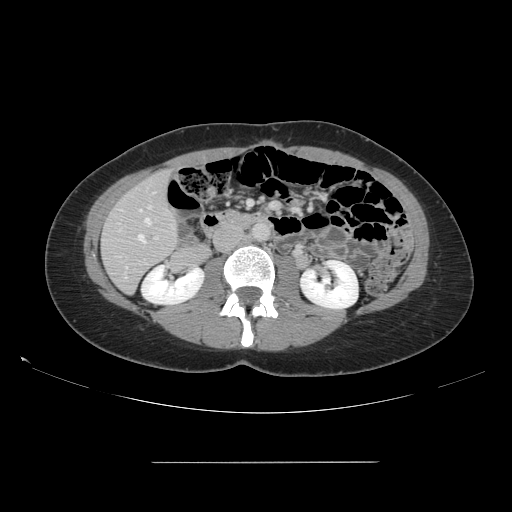
Contrast-enhanced abdominal CT, one axial slice. Slice 54 of 151 in the series (ordered by position). 120 kVp. Soft-tissue window (W 400 / L 40 HU). 512 × 512 image matrix. Female patient, age 46 years. From the clinical record (not read from this slice): diagnosis: colorectal cancer liver metastases, imaged before liver resection; multiple liver metastases: yes; largest metastasis: 3 cm; disease in both lobes: yes.
Structures marked on this image (expert manual segmentation):
- hepatic veins: bounding box (x1, y1, x2, y2) in pixels: (138, 210, 151, 242)
- liver: (102, 171, 178, 292)
- planned liver remnant (the part of the liver to remain after resection): (103, 171, 178, 292)
- portal vein (with intrahepatic branches): (155, 237, 158, 239)